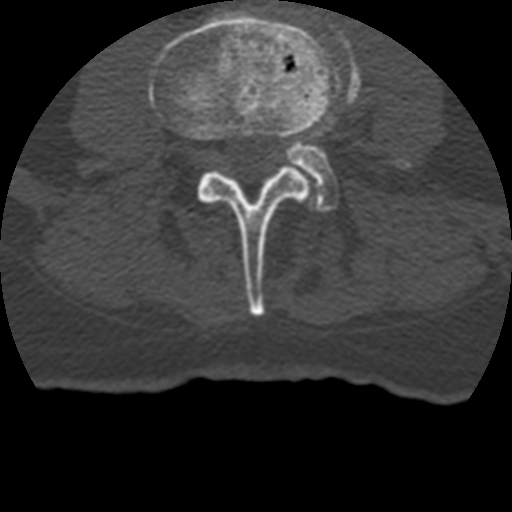
CT including the spine, one axial slice; slice 81 of 399 in the series (ordered by position); 120 kVp; bone window (W 1800 / L 400 HU); 1.25 mm slice thickness; 512 × 512 image matrix. Patient age 69 years. Case-level facts recorded for this patient, not image findings: primary cancer: prostate.
Structures marked on this image (semi-automatic segmentation, software-assisted and operator-edited):
- L3 vertebra: box from (x=148, y=8) to (x=338, y=317) px
- L4 vertebra: (x=286, y=61)–(x=416, y=213)